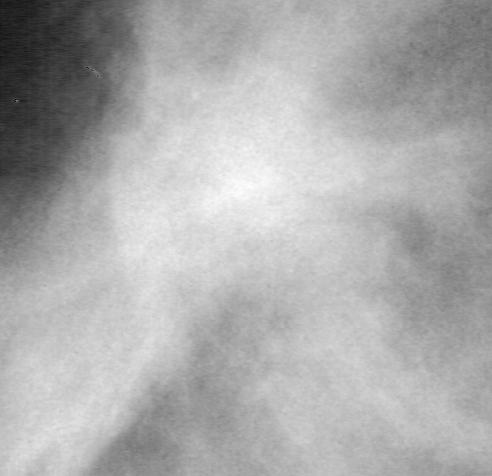
Region of interest cut from a scanned film mammogram (one marked finding), left breast, MLO view.
Marked abnormality: mass, shape irregular, margins spiculated; BI-RADS assessment category 5; subtlety rating 2 on a 1 (subtle) to 5 (obvious) scale; pathology result (as recorded, not read from the image): malignant.